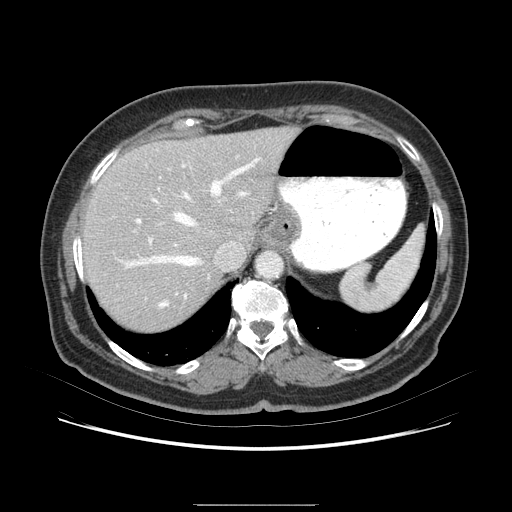
Contrast-enhanced abdominal CT (liver protocol), one axial slice. Soft-tissue window (W 400 / L 40 HU). 2.5 mm slice thickness. 512 × 512 image matrix, field of view 380 × 380 mm. From the clinical record (not read from this slice): diagnosis: hepatocellular carcinoma (patient treated with transarterial chemoembolisation; whether this scan precedes or follows treatment is not stated here); TNM stage (as recorded): Stage-I; Child-Pugh class: A; tumour differentiation: poorly differentiated.
Structures marked on this image (semi-automatic segmentation, software-assisted and operator-edited):
- liver parenchyma outside the tumour (the mass and vessels are separate outlines, so this box may not span the whole liver): bounding box (x1, y1, x2, y2) in pixels: (82, 132, 302, 314)
- liver vessels: (121, 171, 289, 259)